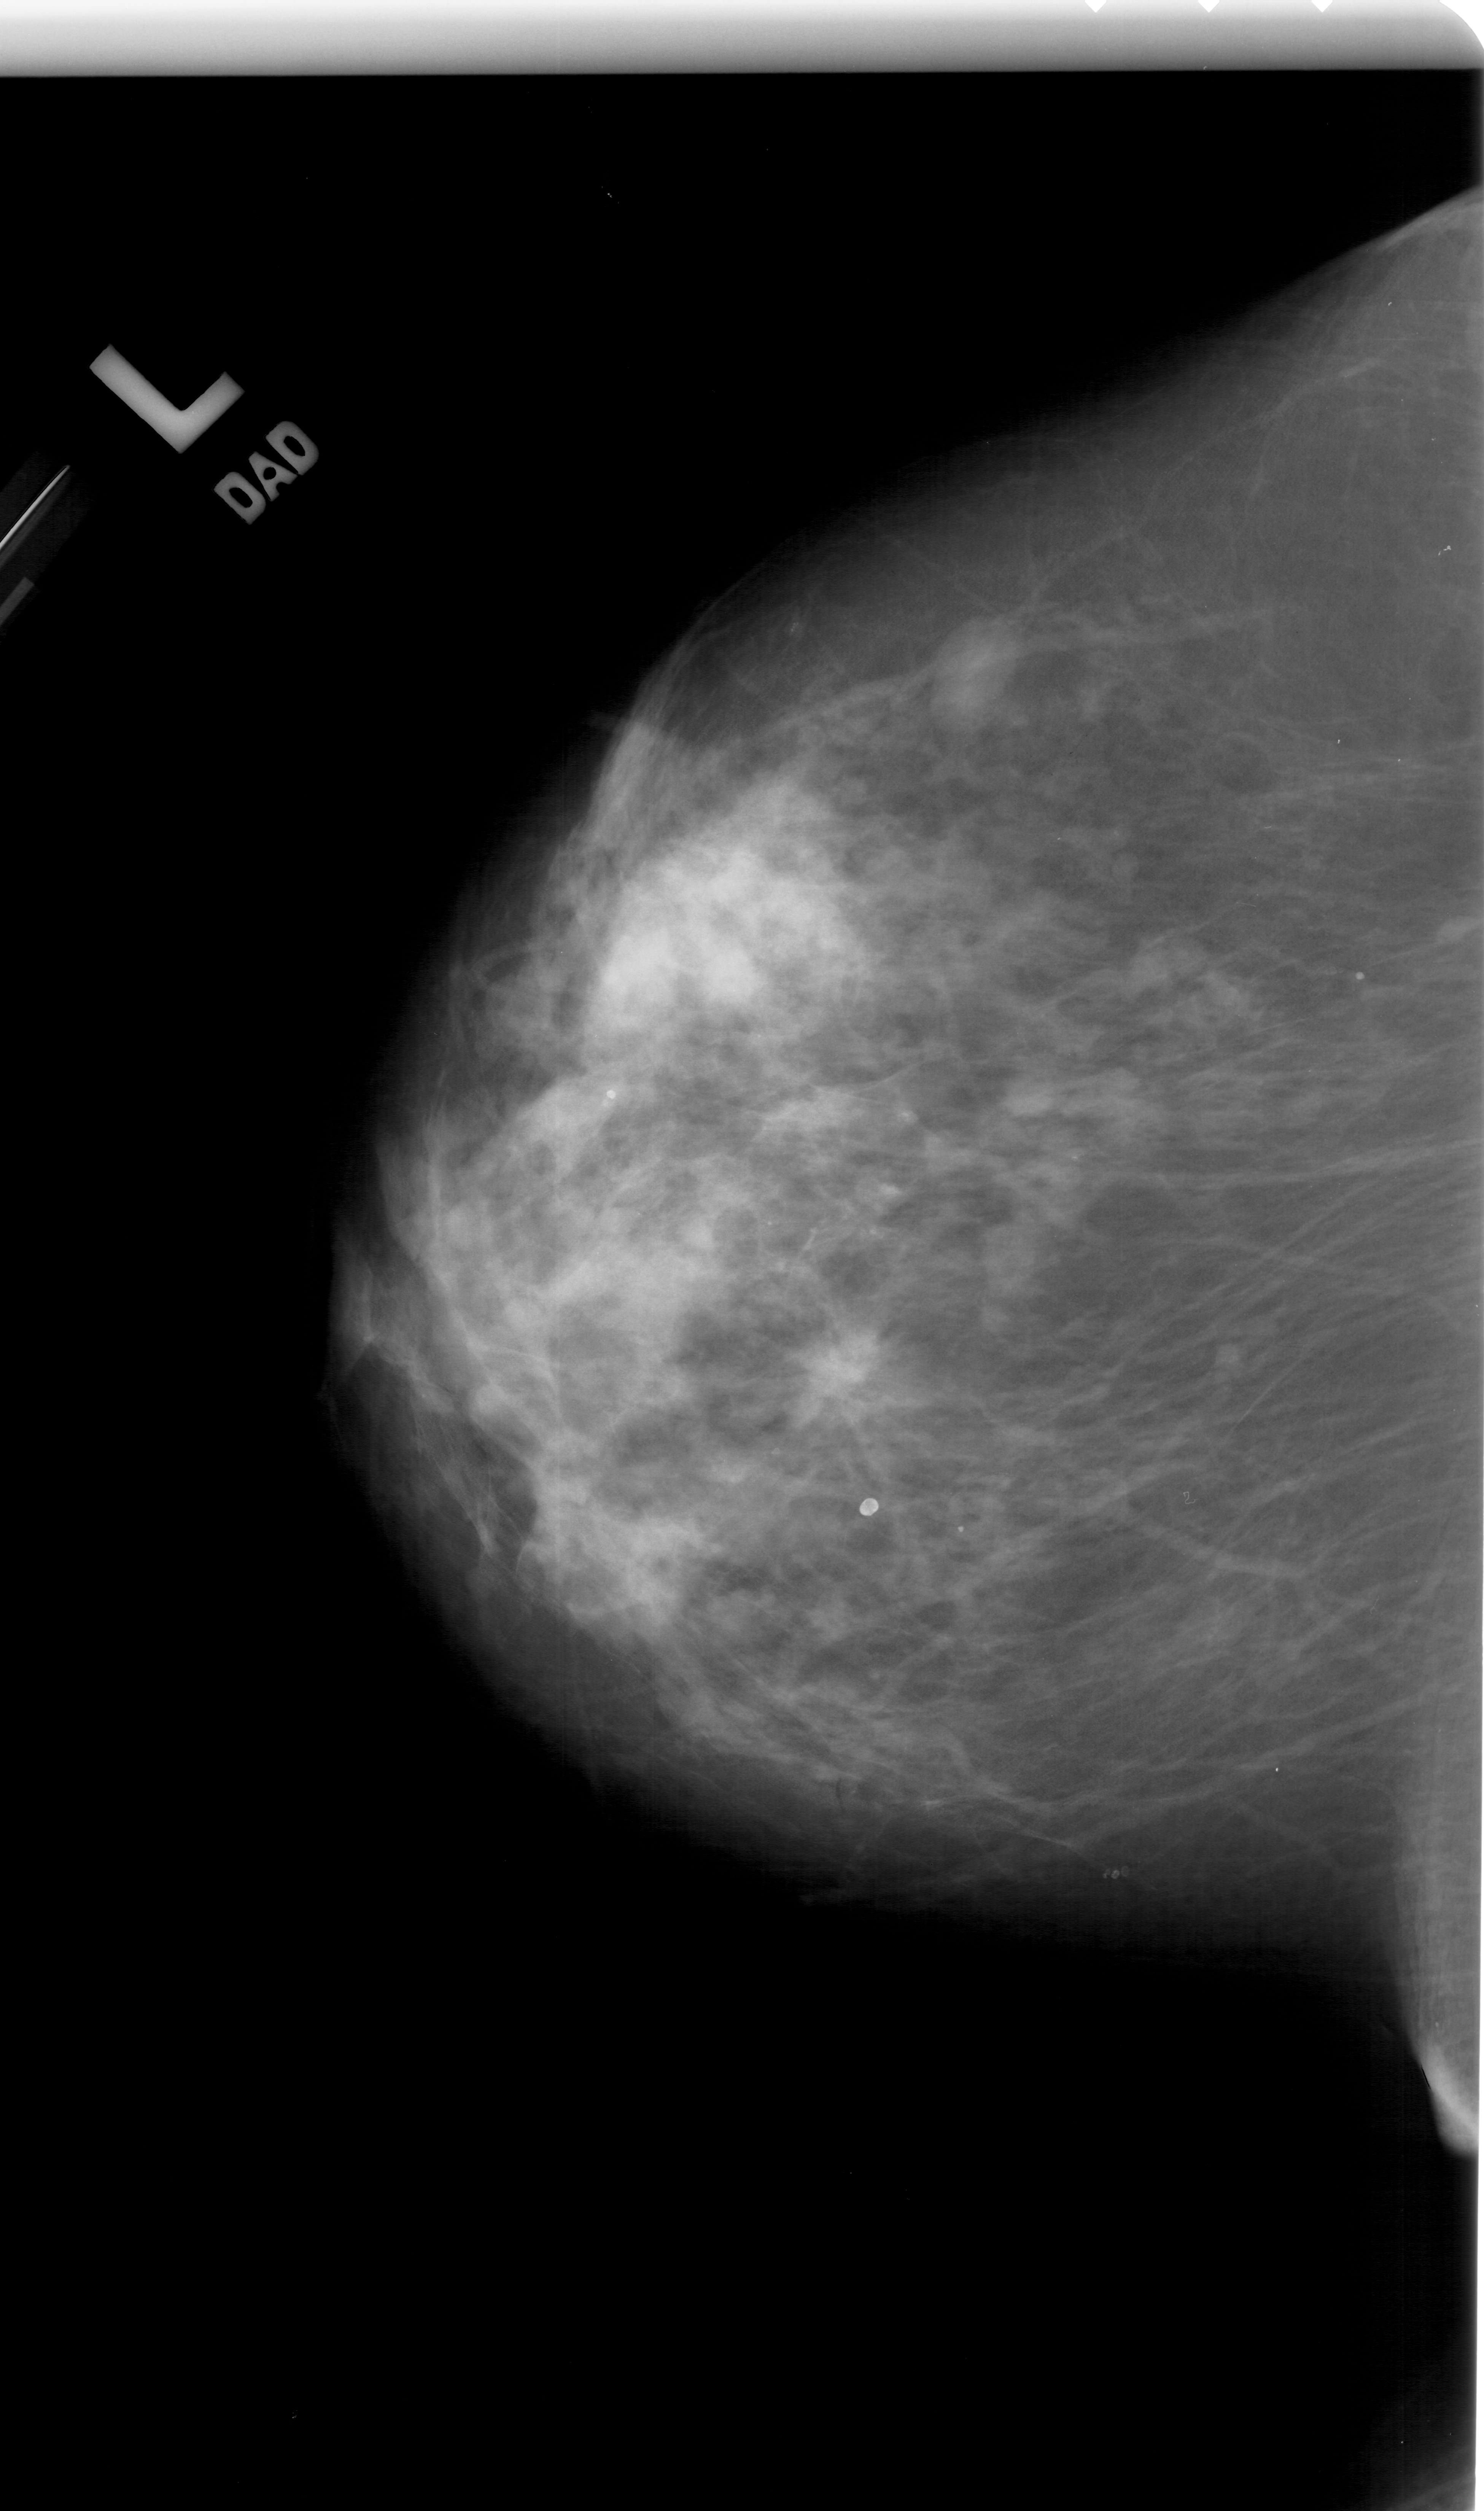
Mammogram (digitized film), left breast, craniocaudal (CC) view, breast composition: heterogeneously dense (BI-RADS density category 3 of 4).
- Finding: mass, shape architectural distortion, margins spiculated; BI-RADS assessment category 5; pathology result (as recorded, not read from the image): malignant.